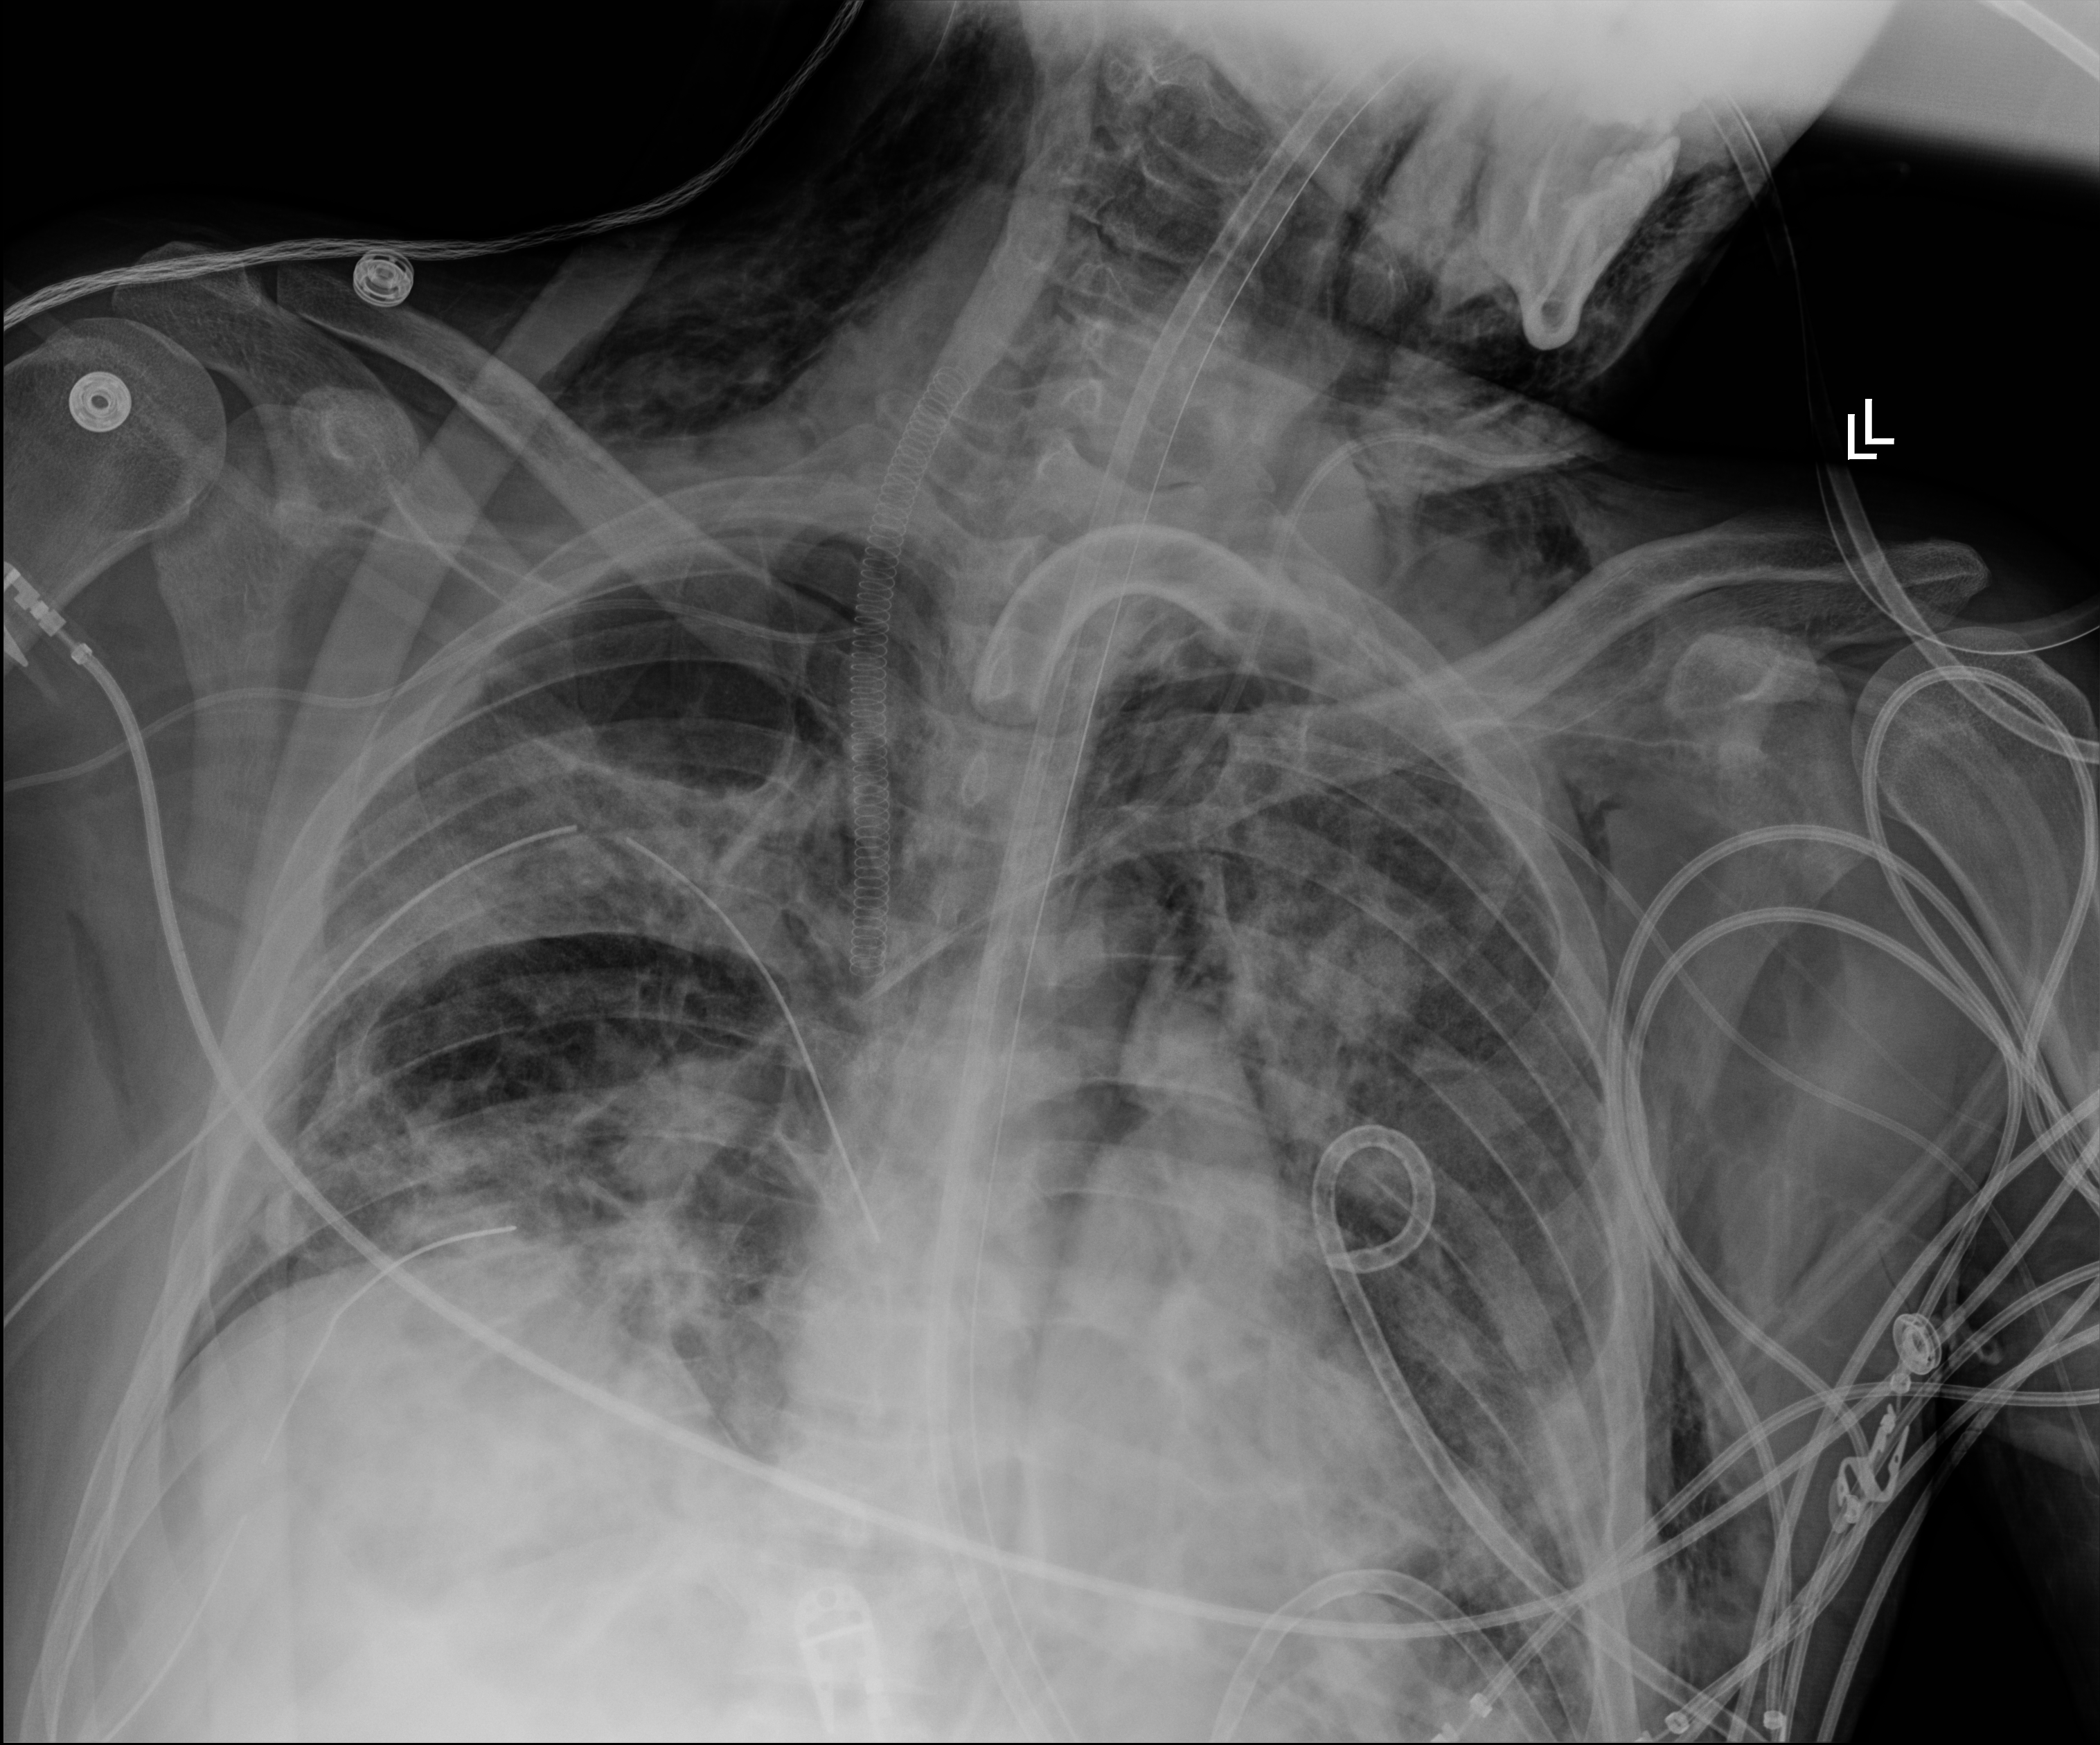
Portable chest radiograph, anteroposterior (AP) projection. Adult patient hospitalised with COVID-19, age 18–59 years.
Hospital-stay facts (about this admission, not read from this image; timing relative to this image not recorded):
- mechanically ventilated during this hospital stay: yes
- admitted to intensive care during this hospital stay: yes